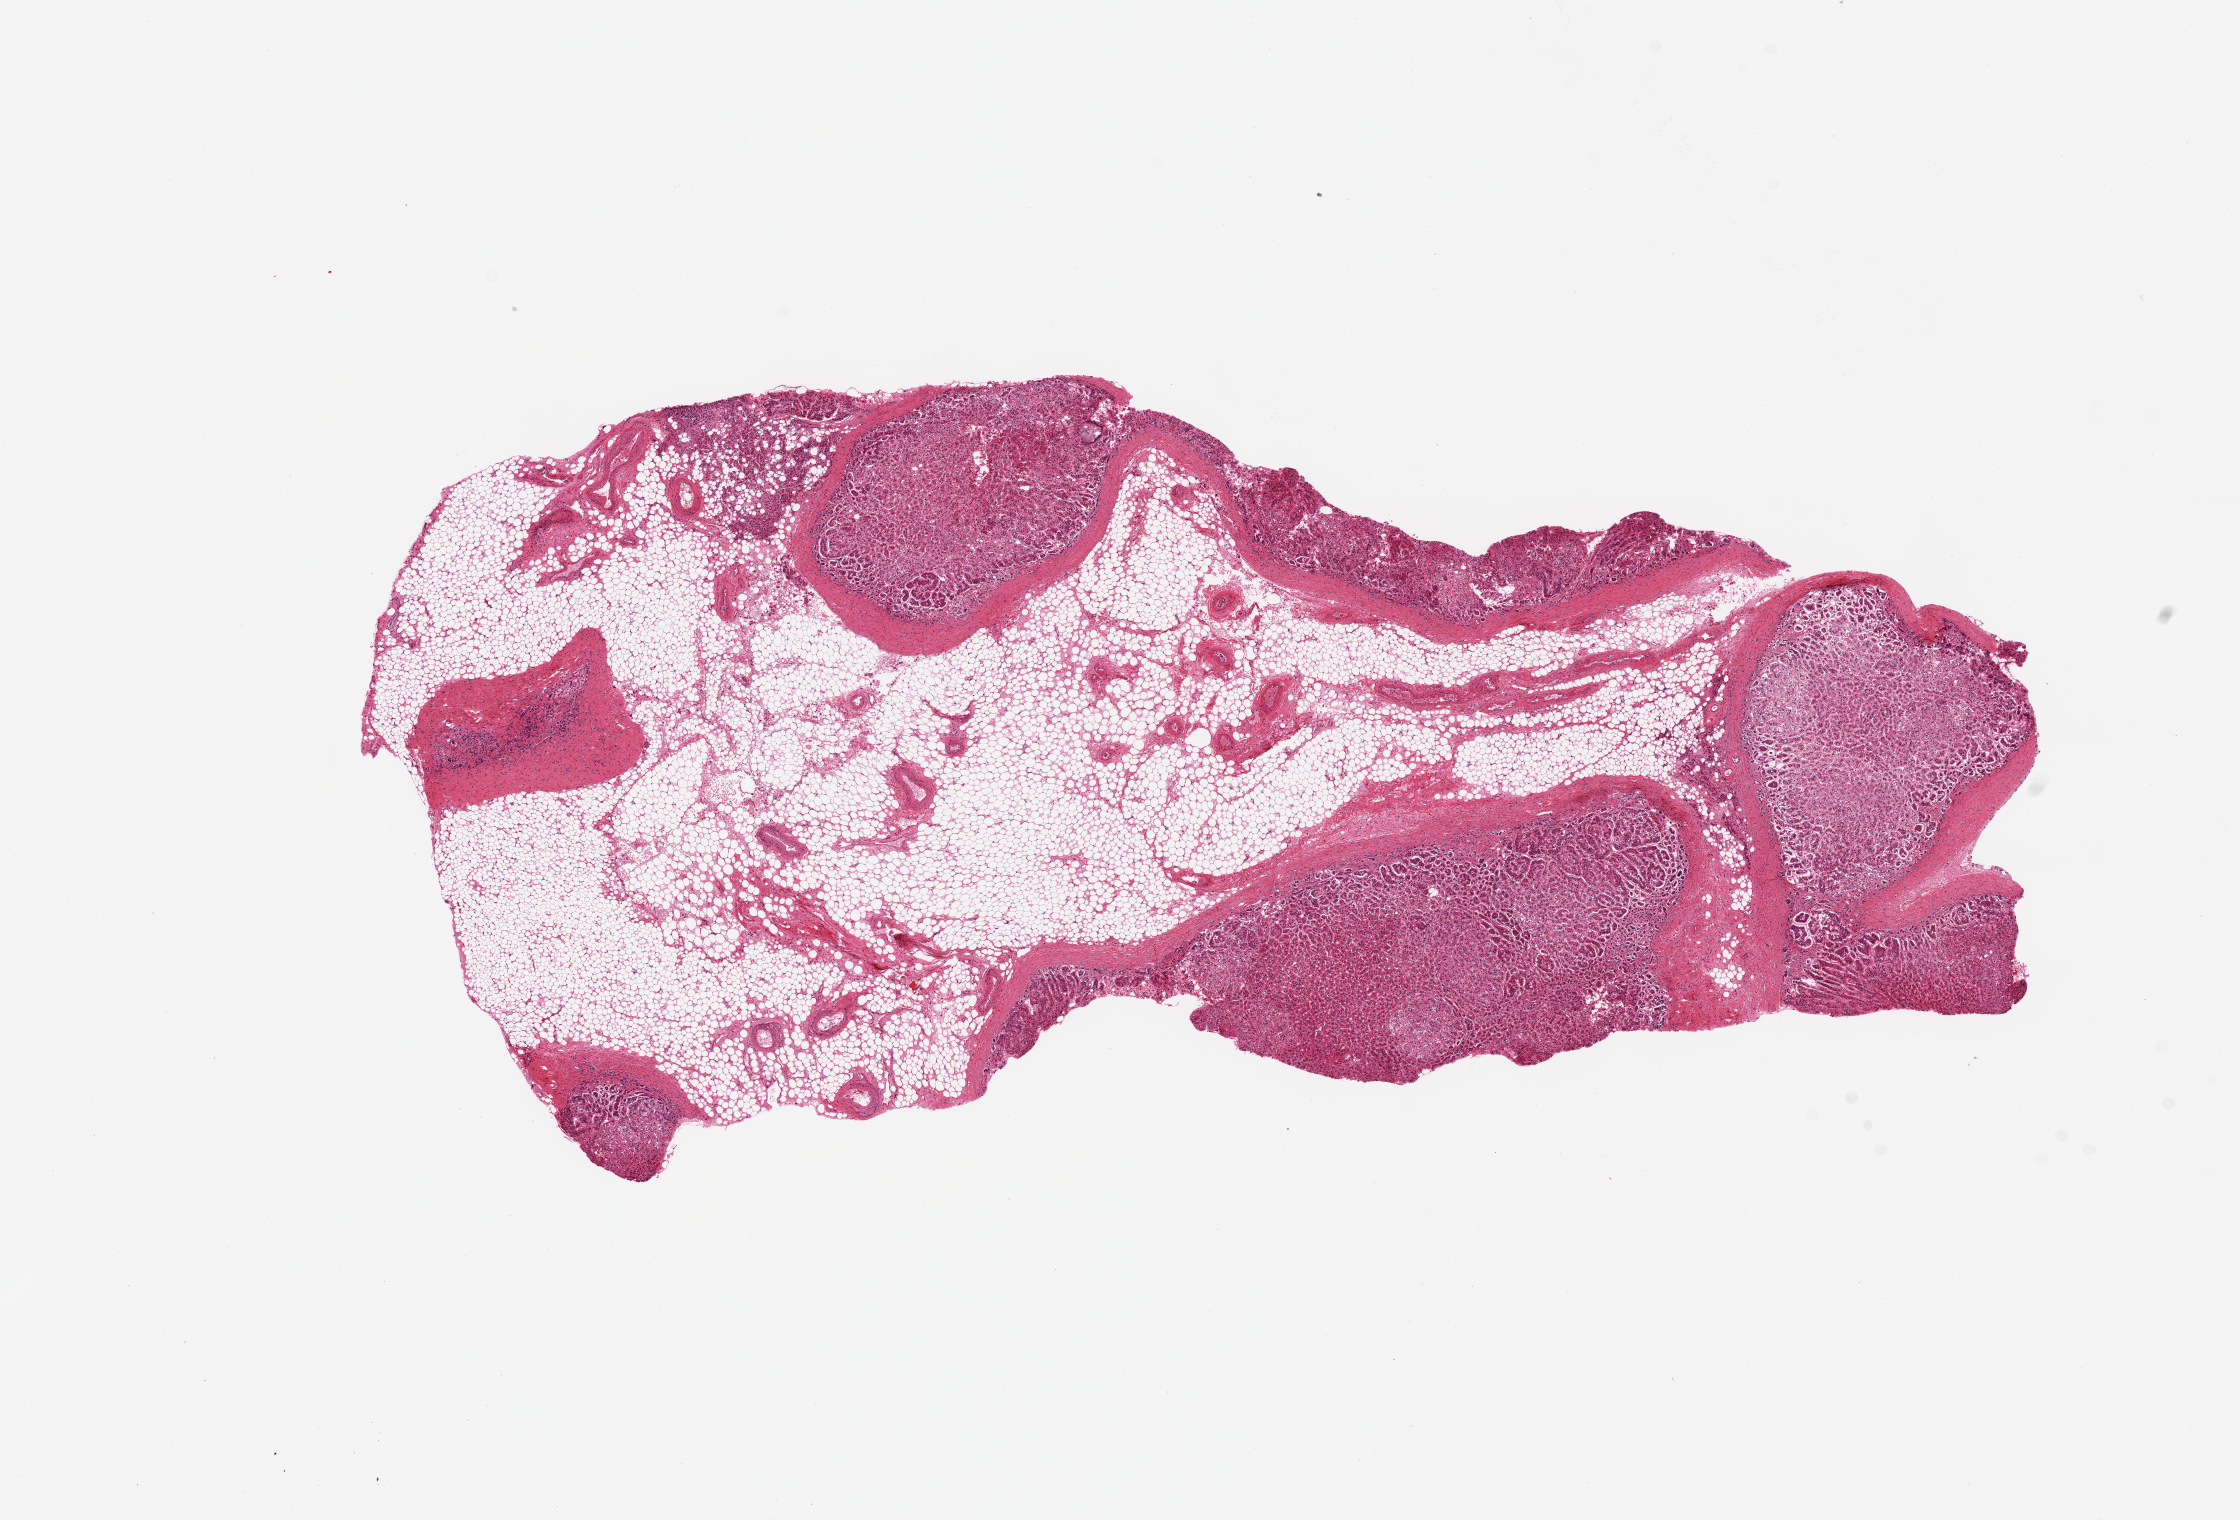
H&E whole-slide image, shown as a low-resolution overview of the whole scanned area (about 17.7 x 12.0 mm), PAXgene-fixed paraffin-embedded (PFPE) section, sampled site (target tissue): adrenal gland, donor tissue sample. Donor: female.
Reviewer comment on this tissue sample: 13x5 mm; cortex; 50% of aliquot is adipose.